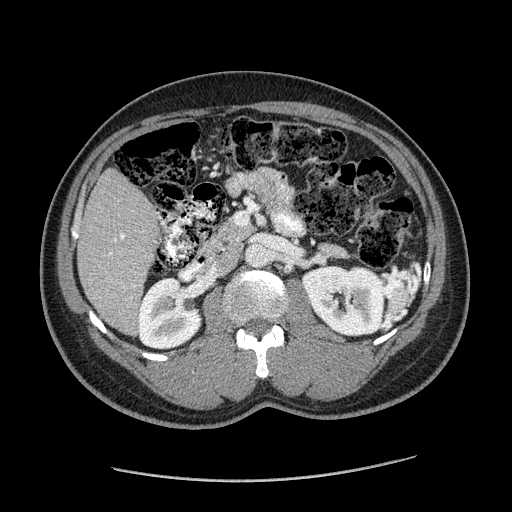
Contrast-enhanced abdominal CT (liver protocol), one axial slice. Slice 69 of 182 in the series (ordered by position). Soft-tissue window (W 400 / L 40 HU). 2.5 mm slice thickness. 512 × 512 image matrix, field of view 400 × 400 mm. Case-level facts recorded for this patient, not image findings: diagnosis: hepatocellular carcinoma (patient treated with transarterial chemoembolisation; whether this scan precedes or follows treatment is not stated here); TNM stage (as recorded): Stage-I; Child-Pugh class: A; tumour nodularity: uninodular.
Outlined on this slice (semi-automatic segmentation, software-assisted and operator-edited):
- liver parenchyma outside the tumour (the mass and vessels are separate outlines, so this box may not span the whole liver): box from (x=78, y=168) to (x=158, y=332) px
- liver vessels: (x=110, y=234)–(x=124, y=255)